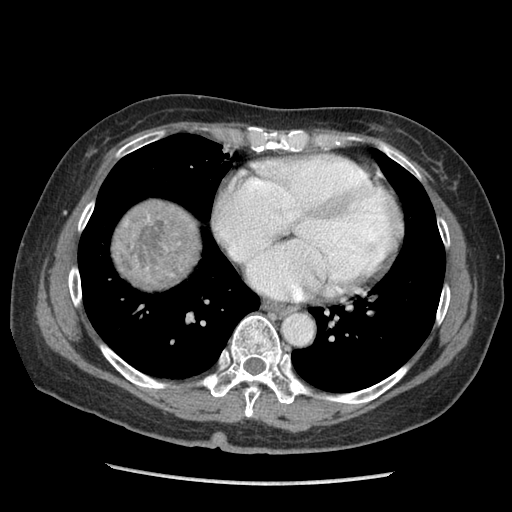
Contrast-enhanced abdominal CT (liver protocol), one axial slice. Slice 96 of 105 in the series (ordered by position). Reconstruction kernel STANDARD. 140 kVp. Soft-tissue window (W 400 / L 40 HU). 512 × 512 image matrix, field of view 340 × 340 mm. Case-level facts recorded for this patient, not image findings: diagnosis: hepatocellular carcinoma (patient treated with transarterial chemoembolisation; whether this scan precedes or follows treatment is not stated here); TNM stage (as recorded): Stage-I; Child-Pugh class: A; tumour differentiation: moderately differentiated.
Annotated regions visible in this slice (semi-automatically segmented with operator editing):
- liver parenchyma outside the tumour (the mass and vessels are separate outlines, so this box may not span the whole liver): bounding box <115,200,198,287> (left, top, right, bottom; pixels)
- mass: <120,208,188,283>